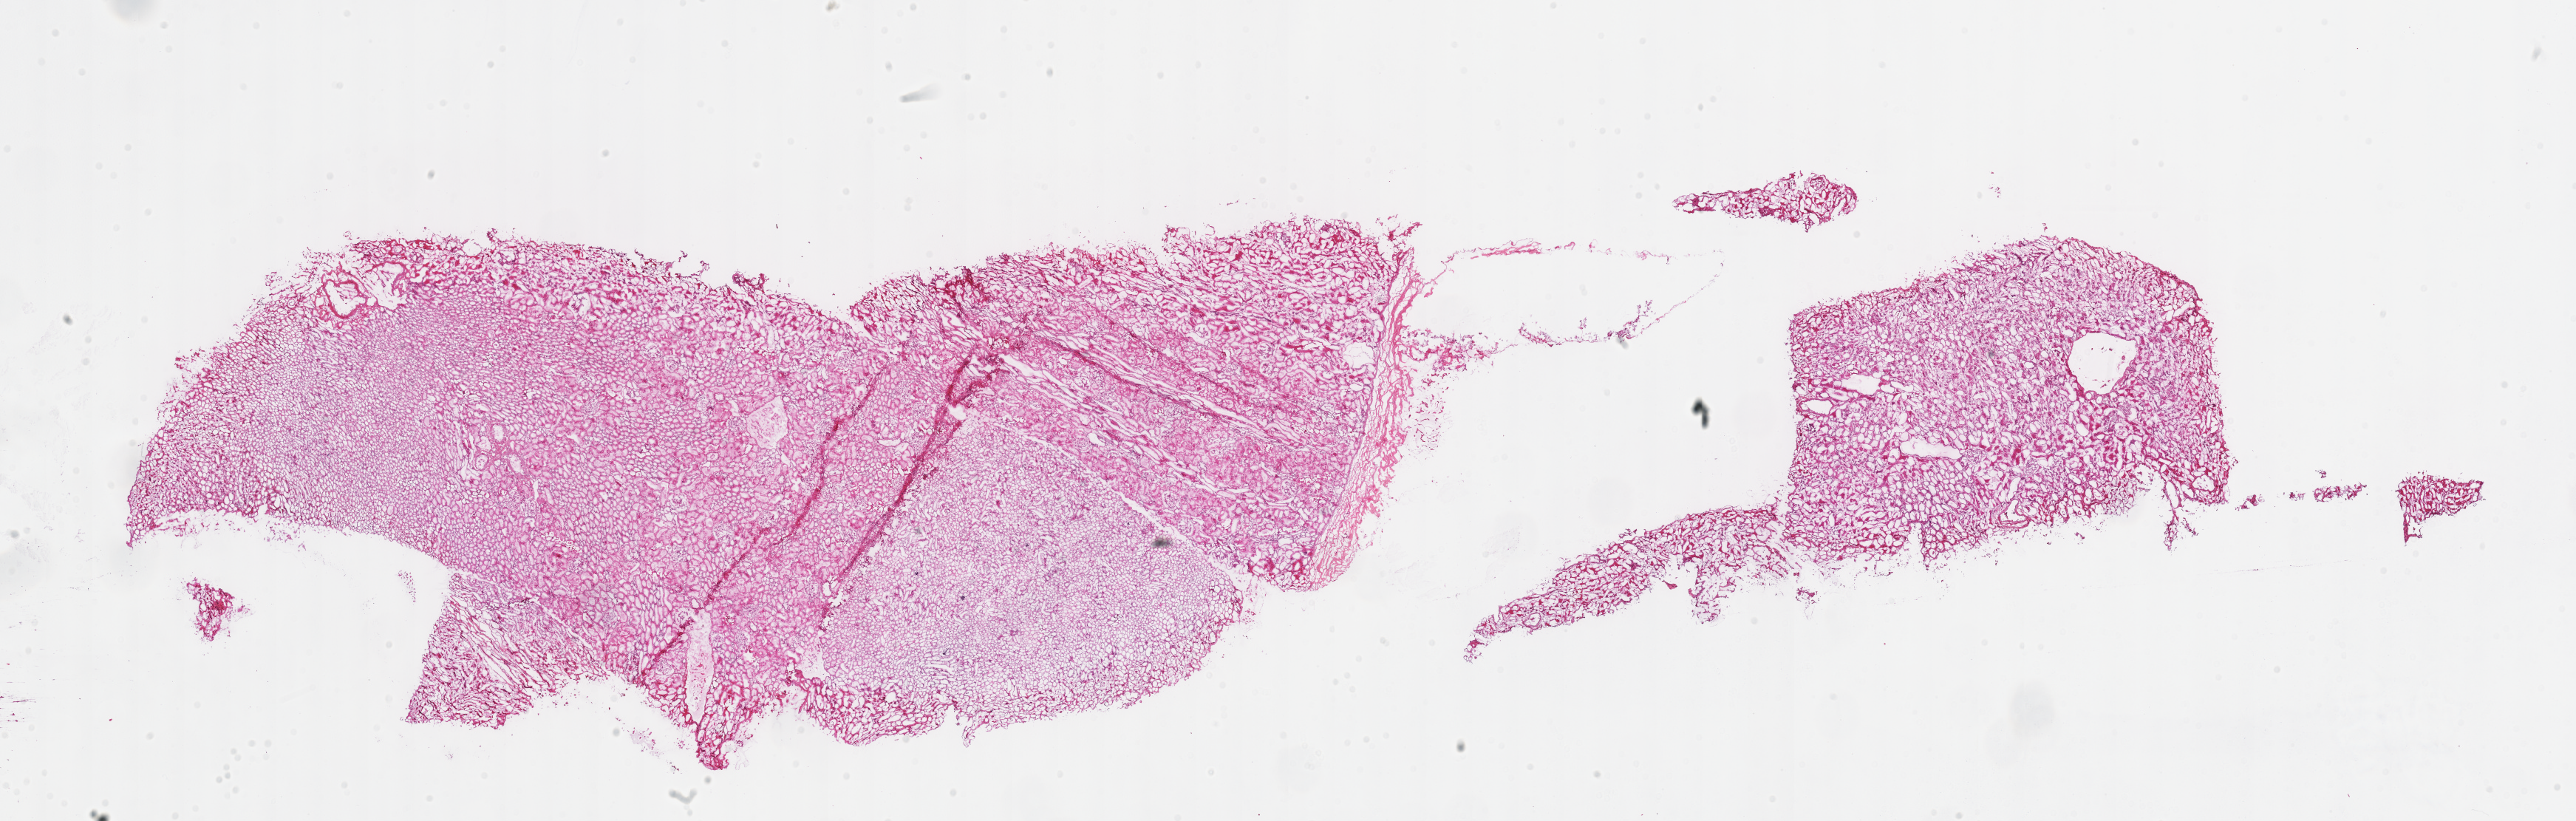
Digitized Hematoxylin and eosin (H&E) stained tissue section (whole slide) — a low-resolution overview of the entire scanned area, about 27.4 x 8.7 mm (from a 40x scan), frozen section from the top of the tissue portion, kidney, solid tissue normal (non-tumour tissue) sample. Female, age 30 years at initial diagnosis.
This section: solid tissue normal (non-tumour) sample from the same patient. Patient diagnosis: Renal cell carcinoma, chromophobe type.